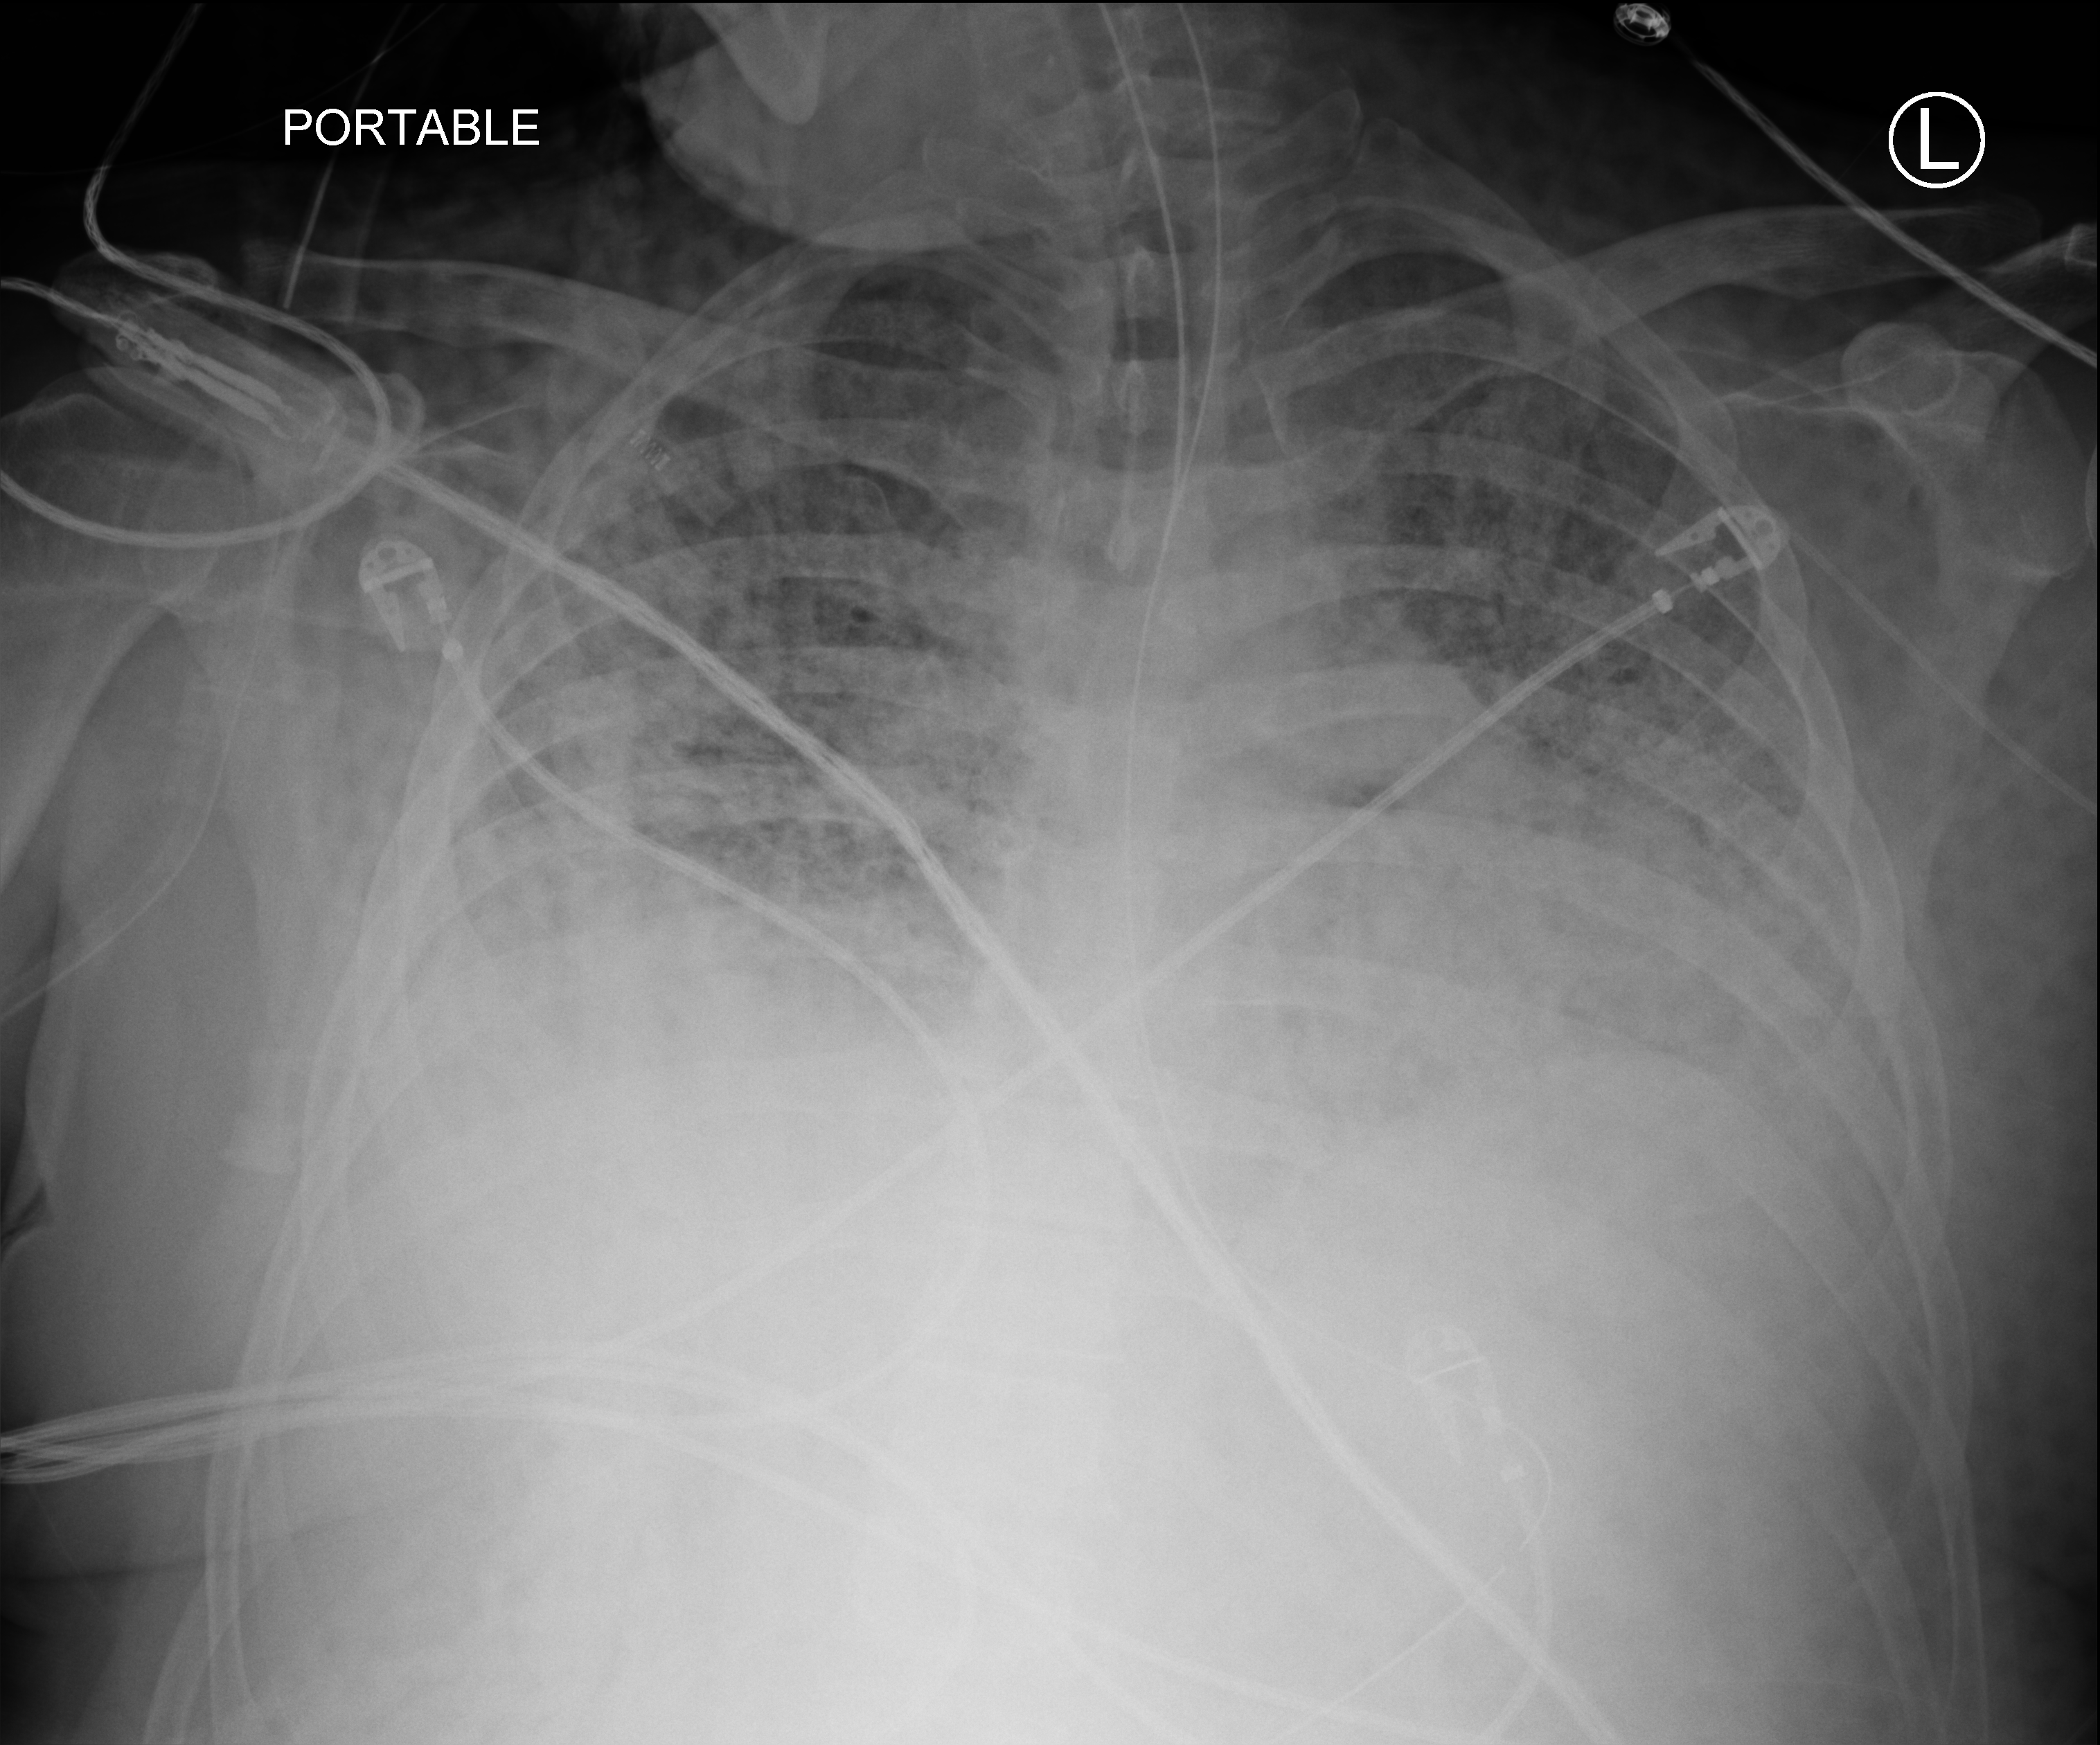
Chest X-ray (portable); anteroposterior (AP) projection. Patient hospitalised with COVID-19; male, aged 18–59 years.
Hospital-stay facts (about this admission, not read from this image; timing relative to this image not recorded): admitted to intensive care during this hospital stay: yes.